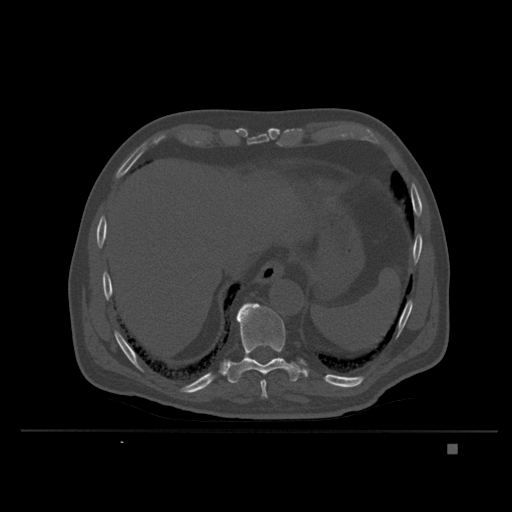
CT including the spine, one axial slice; position 196 of 435 along the scan axis; bone window (W 1800 / L 400 HU); 512 × 512 image matrix, field of view 434 × 434 mm. Patient: male, 73 years. Case-level facts recorded for this patient, not image findings: primary cancer: skin.
Outlined on this slice (semi-automatically segmented with operator editing):
- T10 vertebra: bounding box [x1, y1, x2, y2] px = [226, 303, 307, 384]
- T11 vertebra: [237, 310, 240, 315]
- T9 vertebra: [260, 380, 268, 399]